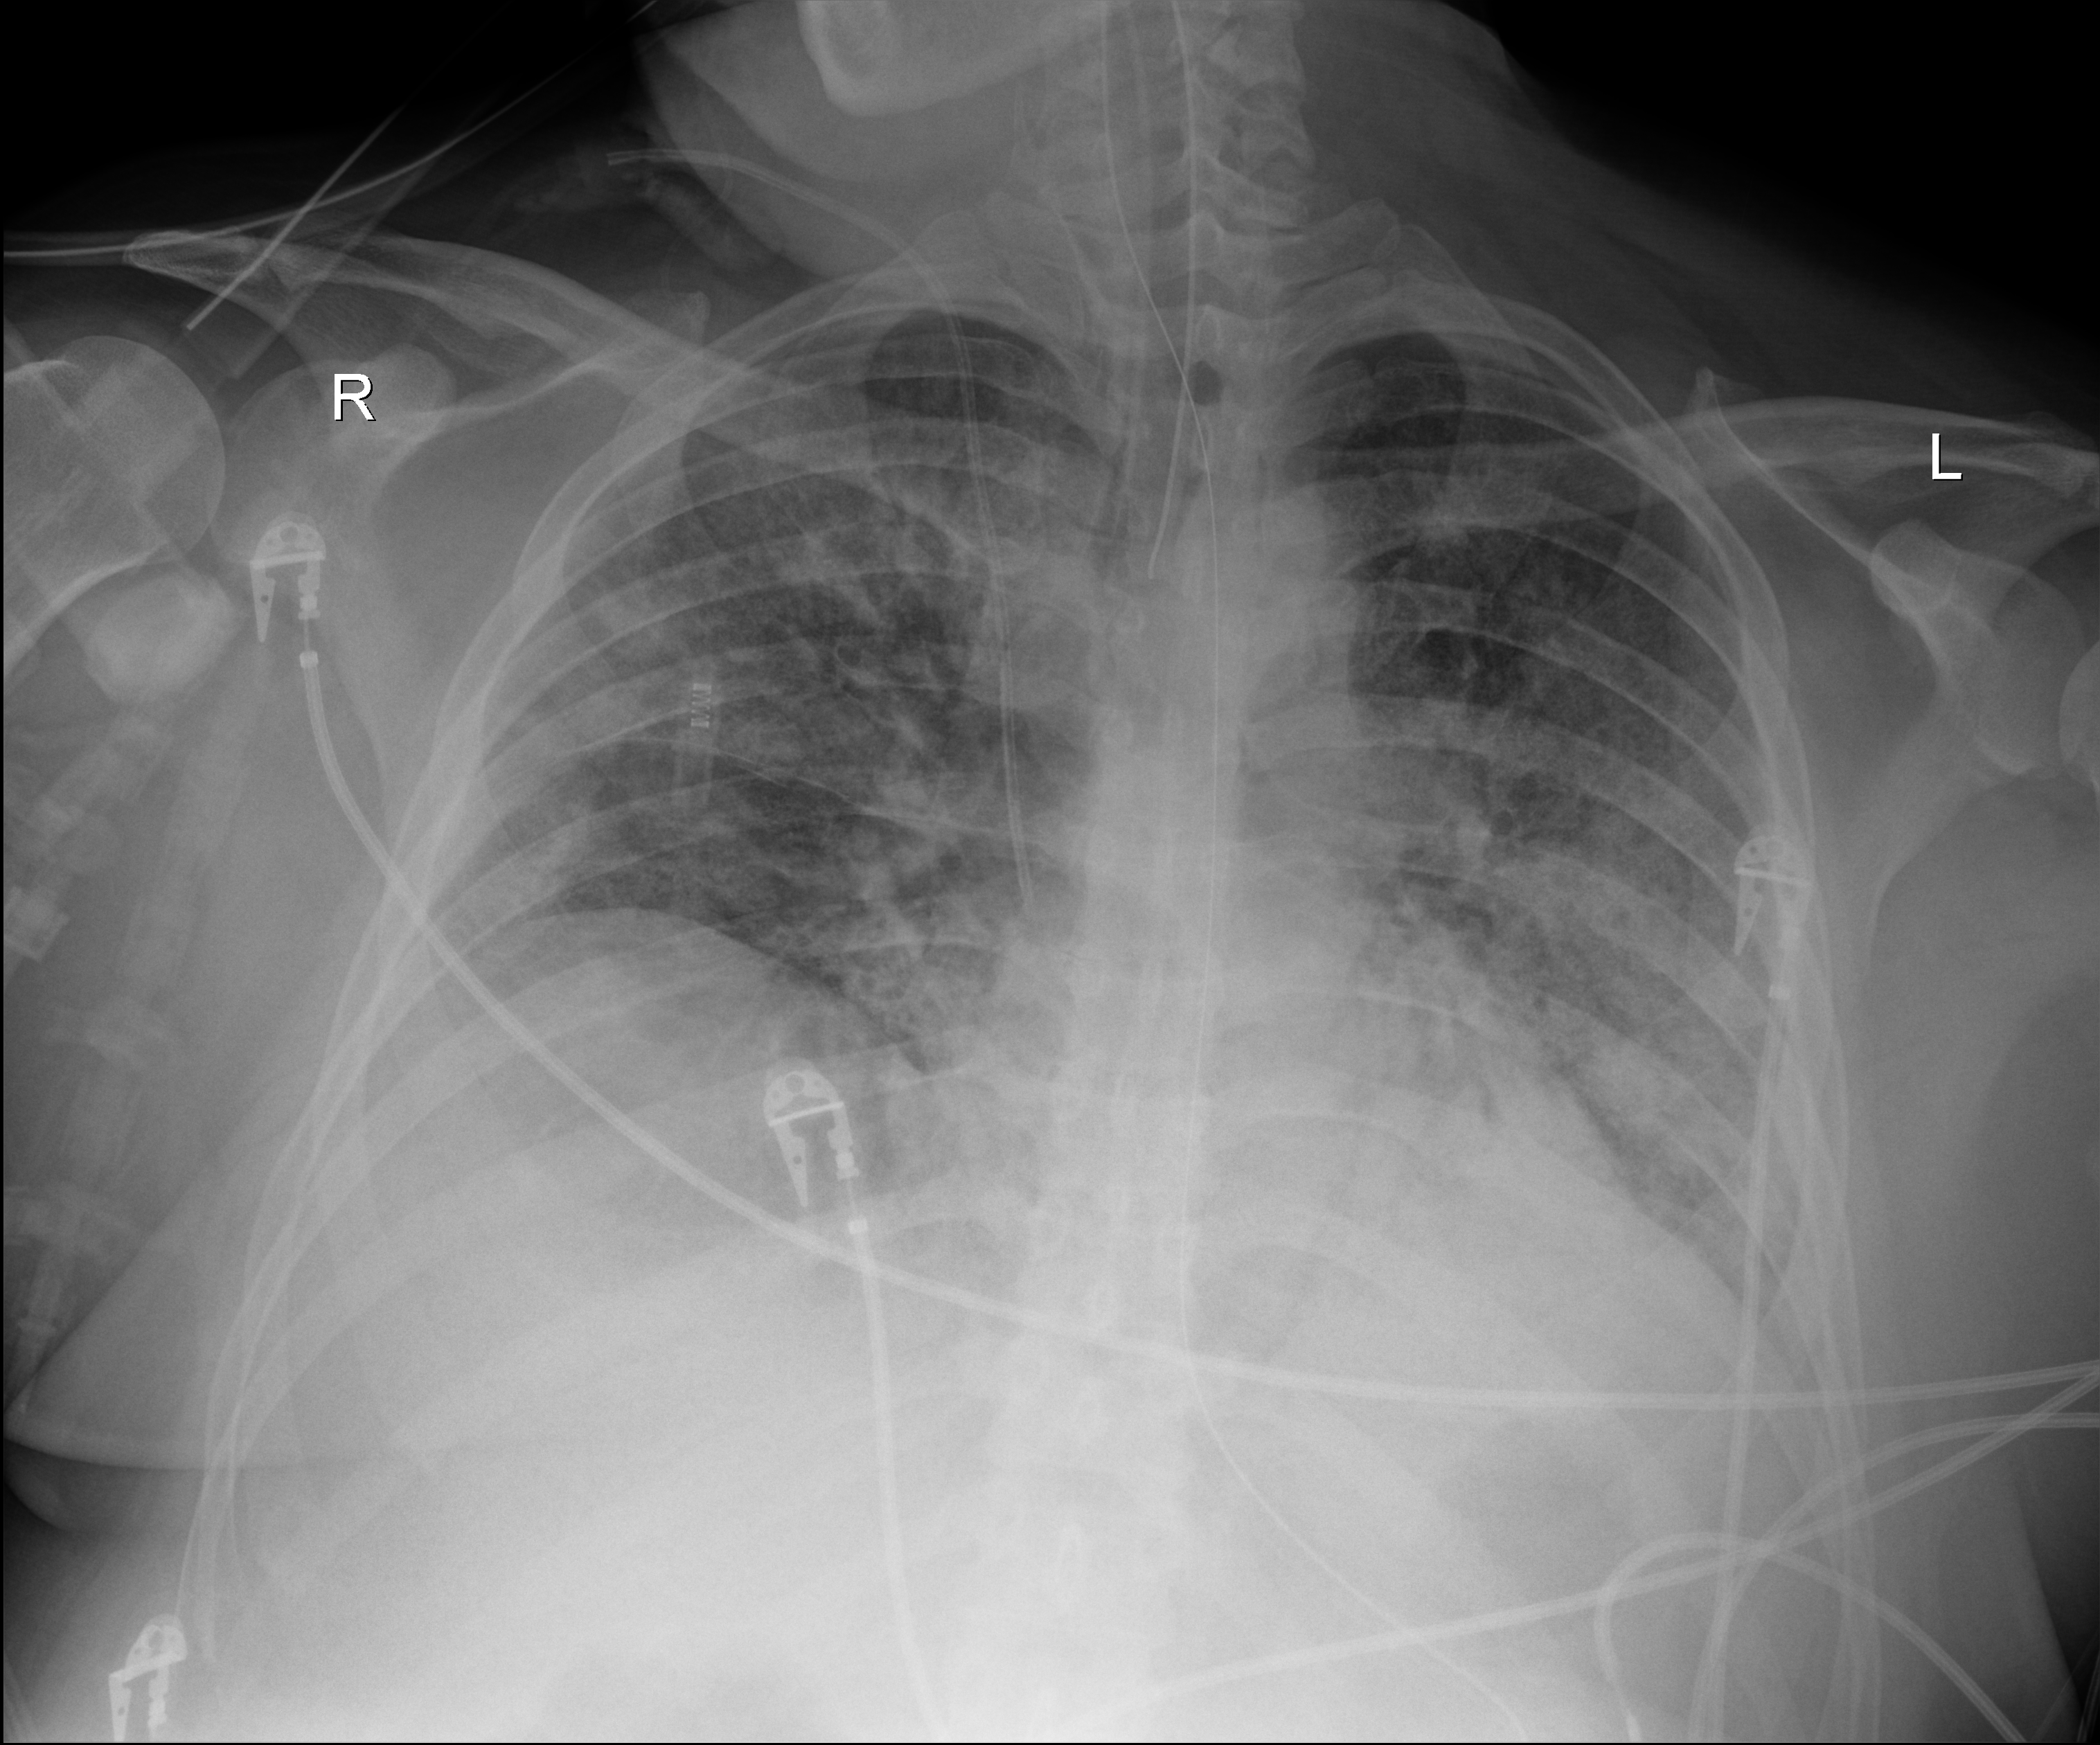
Chest X-ray; anteroposterior (AP) projection. Patient hospitalised with COVID-19; male, aged 18–59 years.
Hospital-stay facts (about this admission, not read from this image; timing relative to this image not recorded):
- admitted to intensive care during this hospital stay: yes
- mechanically ventilated during this hospital stay: yes